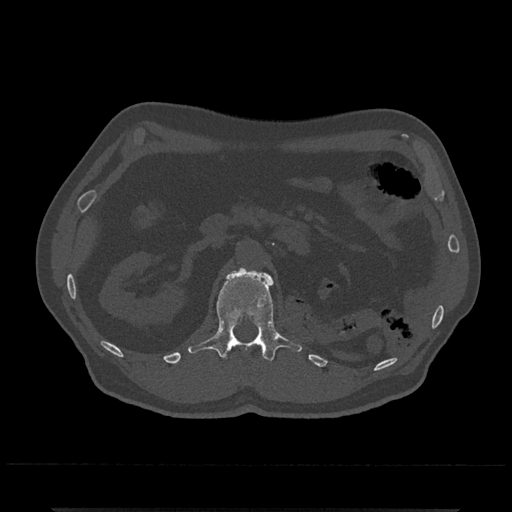
CT including the spine, one axial slice; slice 366 of 797 in the series (ordered by position); reconstruction kernel Br40s/3; bone window (W 1800 / L 400 HU); 512 × 512 image matrix, field of view 393 × 393 mm. Patient: male, 67 years. From the clinical record (not read from this slice): primary cancer: prostate.
Outlined on this slice (semi-automatically segmented with operator editing):
- L1 vertebra: box from (x=187, y=268) to (x=302, y=361) px